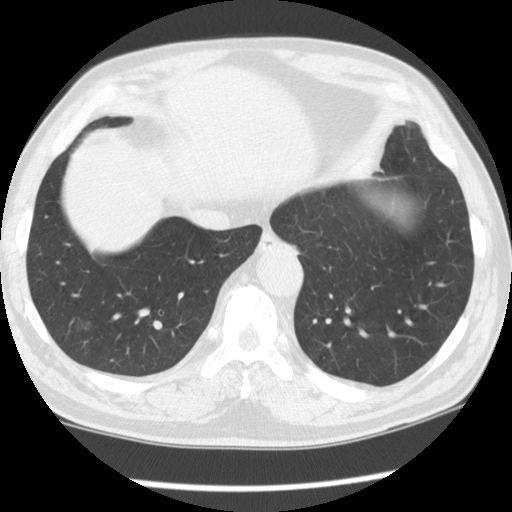
Low-dose screening chest CT, axial slice; baseline annual screen; lung window (W 1500 / L -600 HU); 2.5 mm slice thickness; standard (soft-tissue) reconstruction kernel (STANDARD); slice 89 of 122 in the series; 512 × 512 image matrix, field of view 330 × 330 mm. Male participant, aged 62 years at enrolment. Former smoker at enrolment.
Lesion marked by an expert reader, bounding box <50,302,115,364> (left, top, right, bottom; pixels). Reader record for this screening exam (exam-level; its link to the box is not recorded): non-calcified nodule or mass ≥4 mm, right lower lobe, 13 × 11 mm, smooth margins, ground glass attenuation. Official screen result: positive, change unspecified: nodule(s) >= 4 mm or enlarging nodule(s), mass(es), or other non-specific abnormalities suspicious for lung cancer.